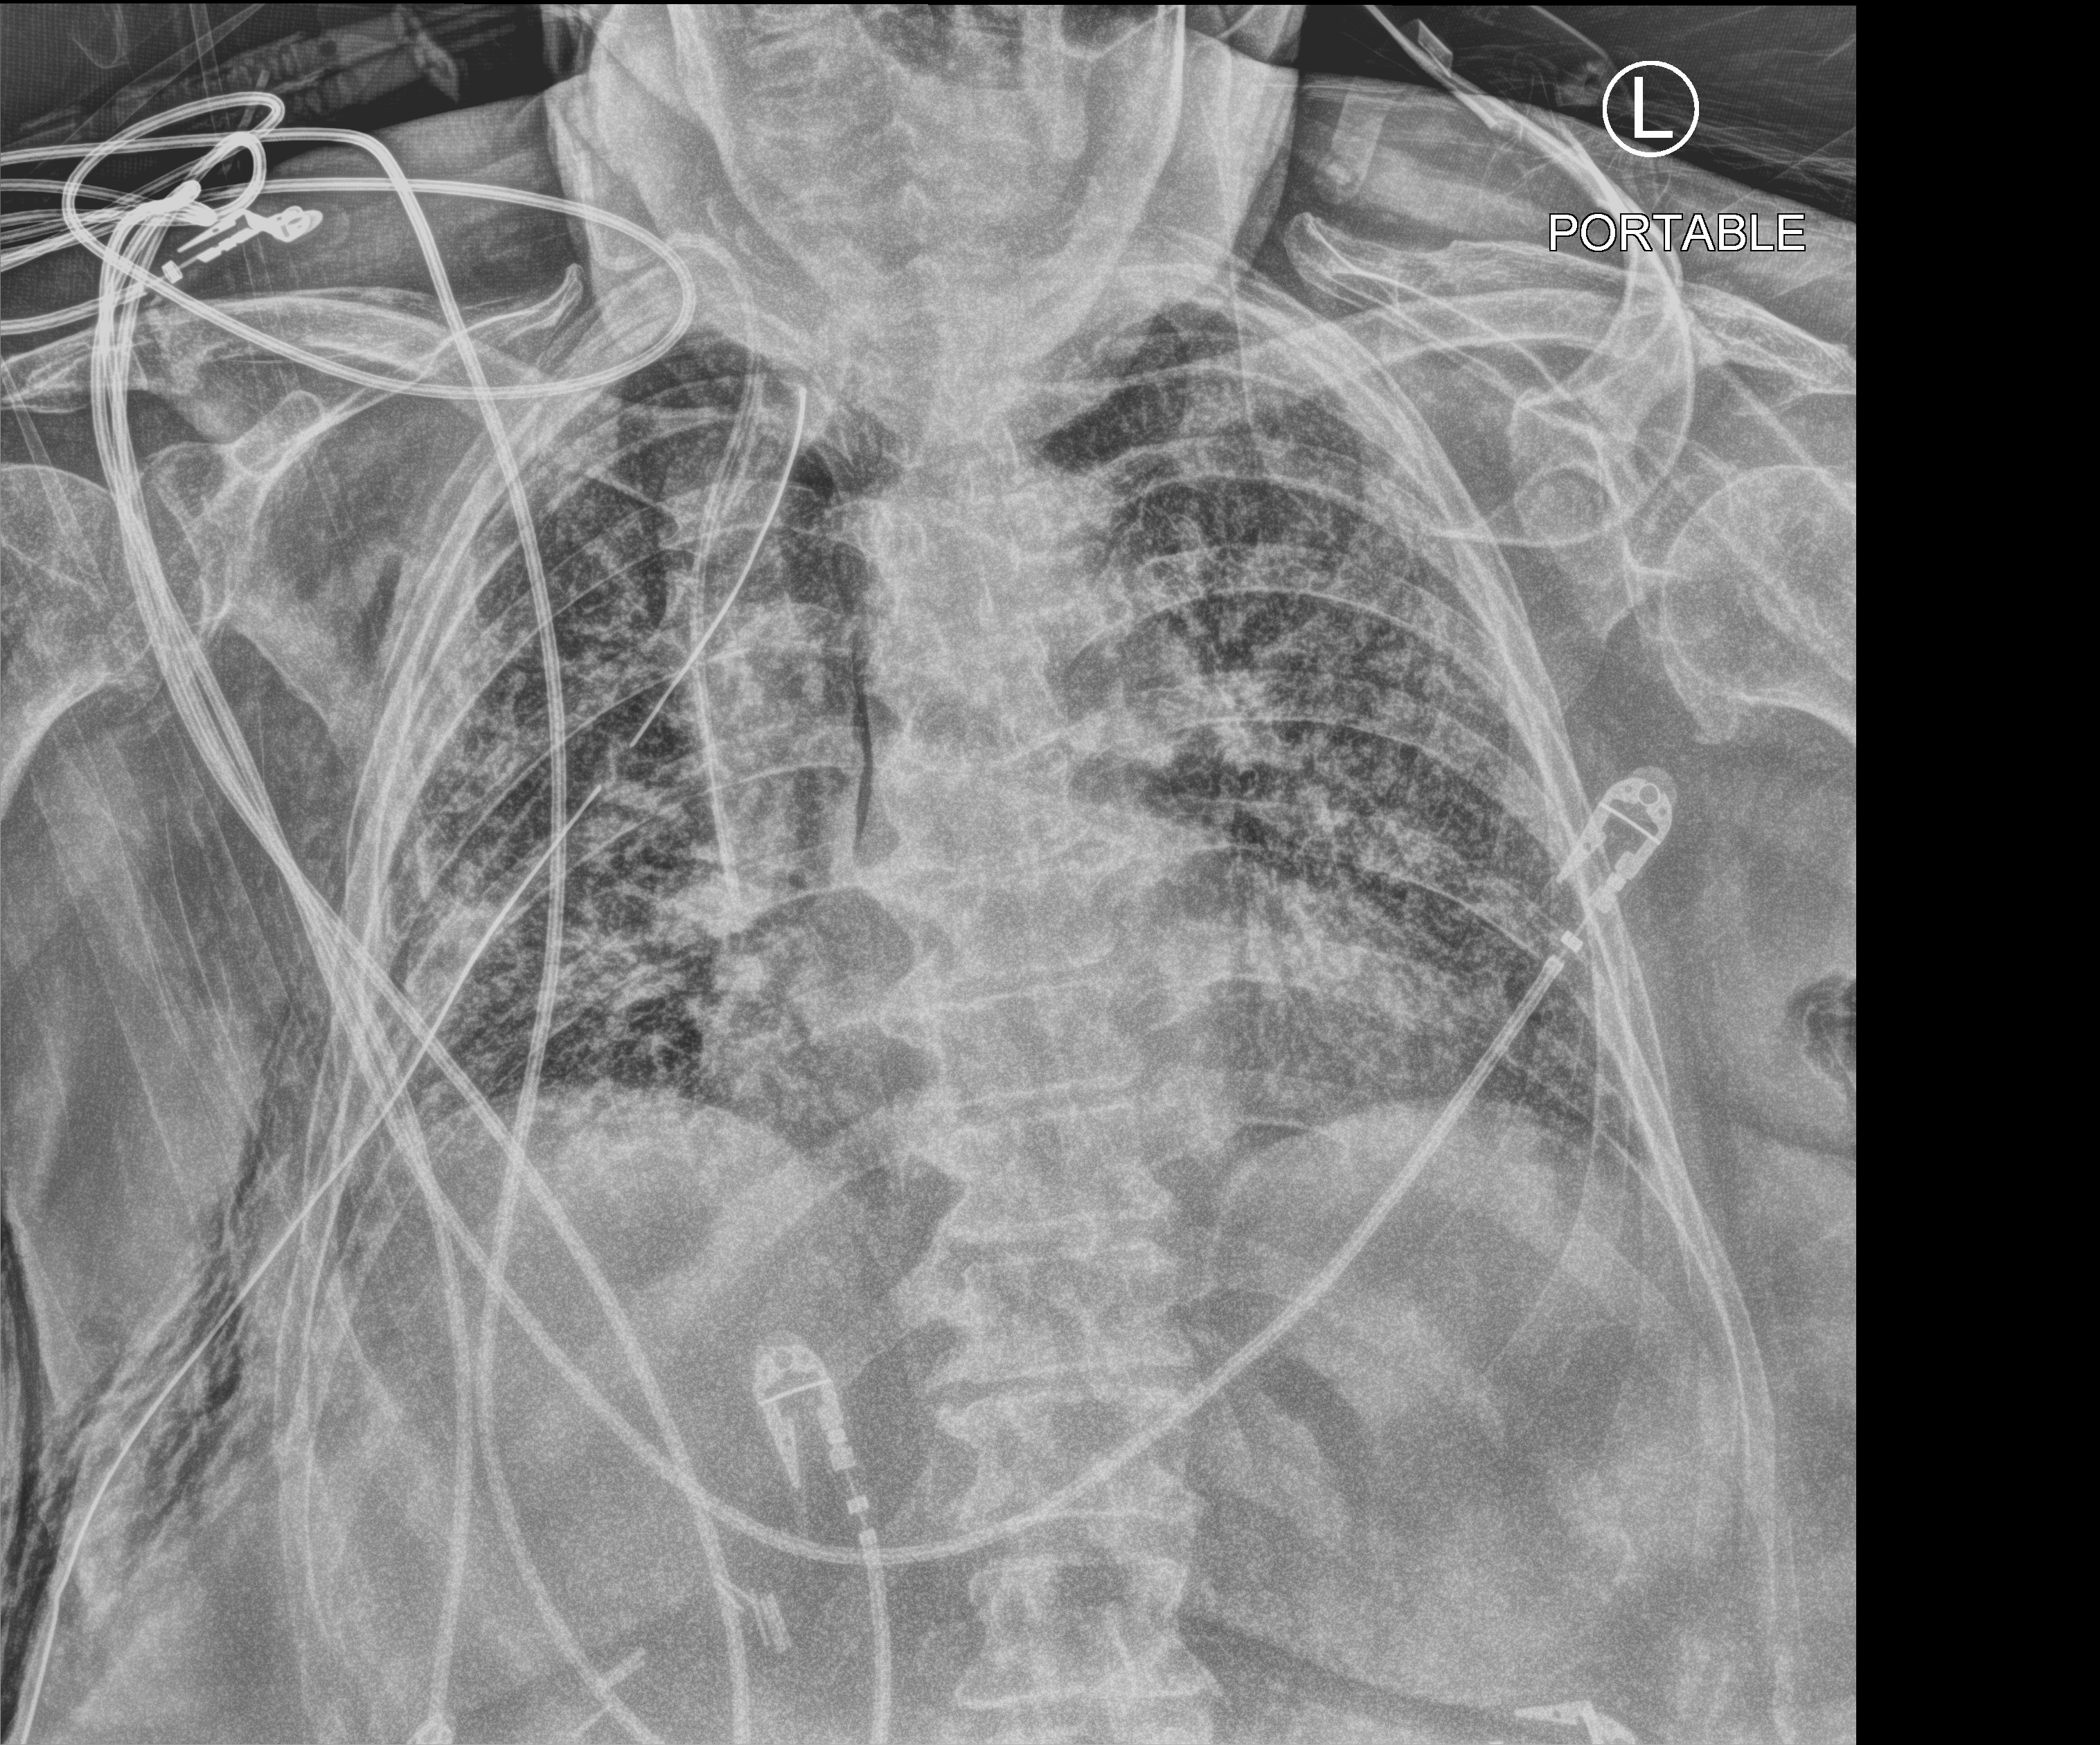
Chest X-ray (portable). Female patient hospitalised with COVID-19, age 75–90 years.
From the hospital-stay record, not from the radiograph (when in the stay this image was taken is not recorded): length of hospital stay: 56 days; admitted to intensive care during this hospital stay: no; COPD (admission record): no.